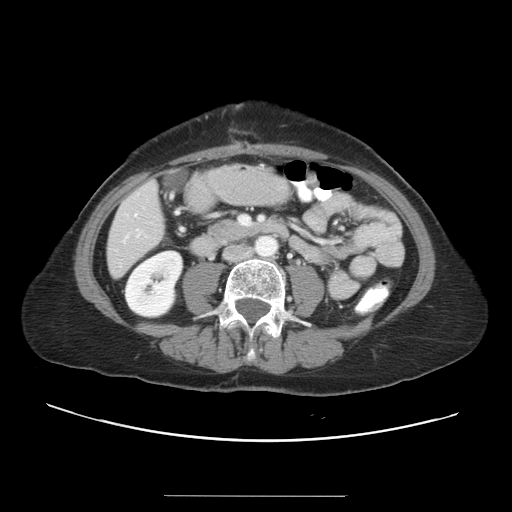
Contrast-enhanced abdominal CT, one axial slice. Slice 5 of 34 in the series (ordered by position). 120 kVp. Intravenous contrast given. Soft-tissue window (W 400 / L 40 HU). 512 × 512 image matrix. Female patient, age 69 years. From the clinical record (not read from this slice): diagnosis: colorectal cancer liver metastases, imaged before liver resection; multiple liver metastases: yes; largest metastasis: 1.4 cm; disease in both lobes: yes.
Outlined on this slice (manually delineated by an expert):
- hepatic veins: bounding box [x1, y1, x2, y2] px = [135, 215, 141, 236]
- liver: [108, 183, 164, 276]
- planned liver remnant (the part of the liver to remain after resection): [108, 226, 163, 276]
- portal vein (with intrahepatic branches): [240, 216, 249, 225]